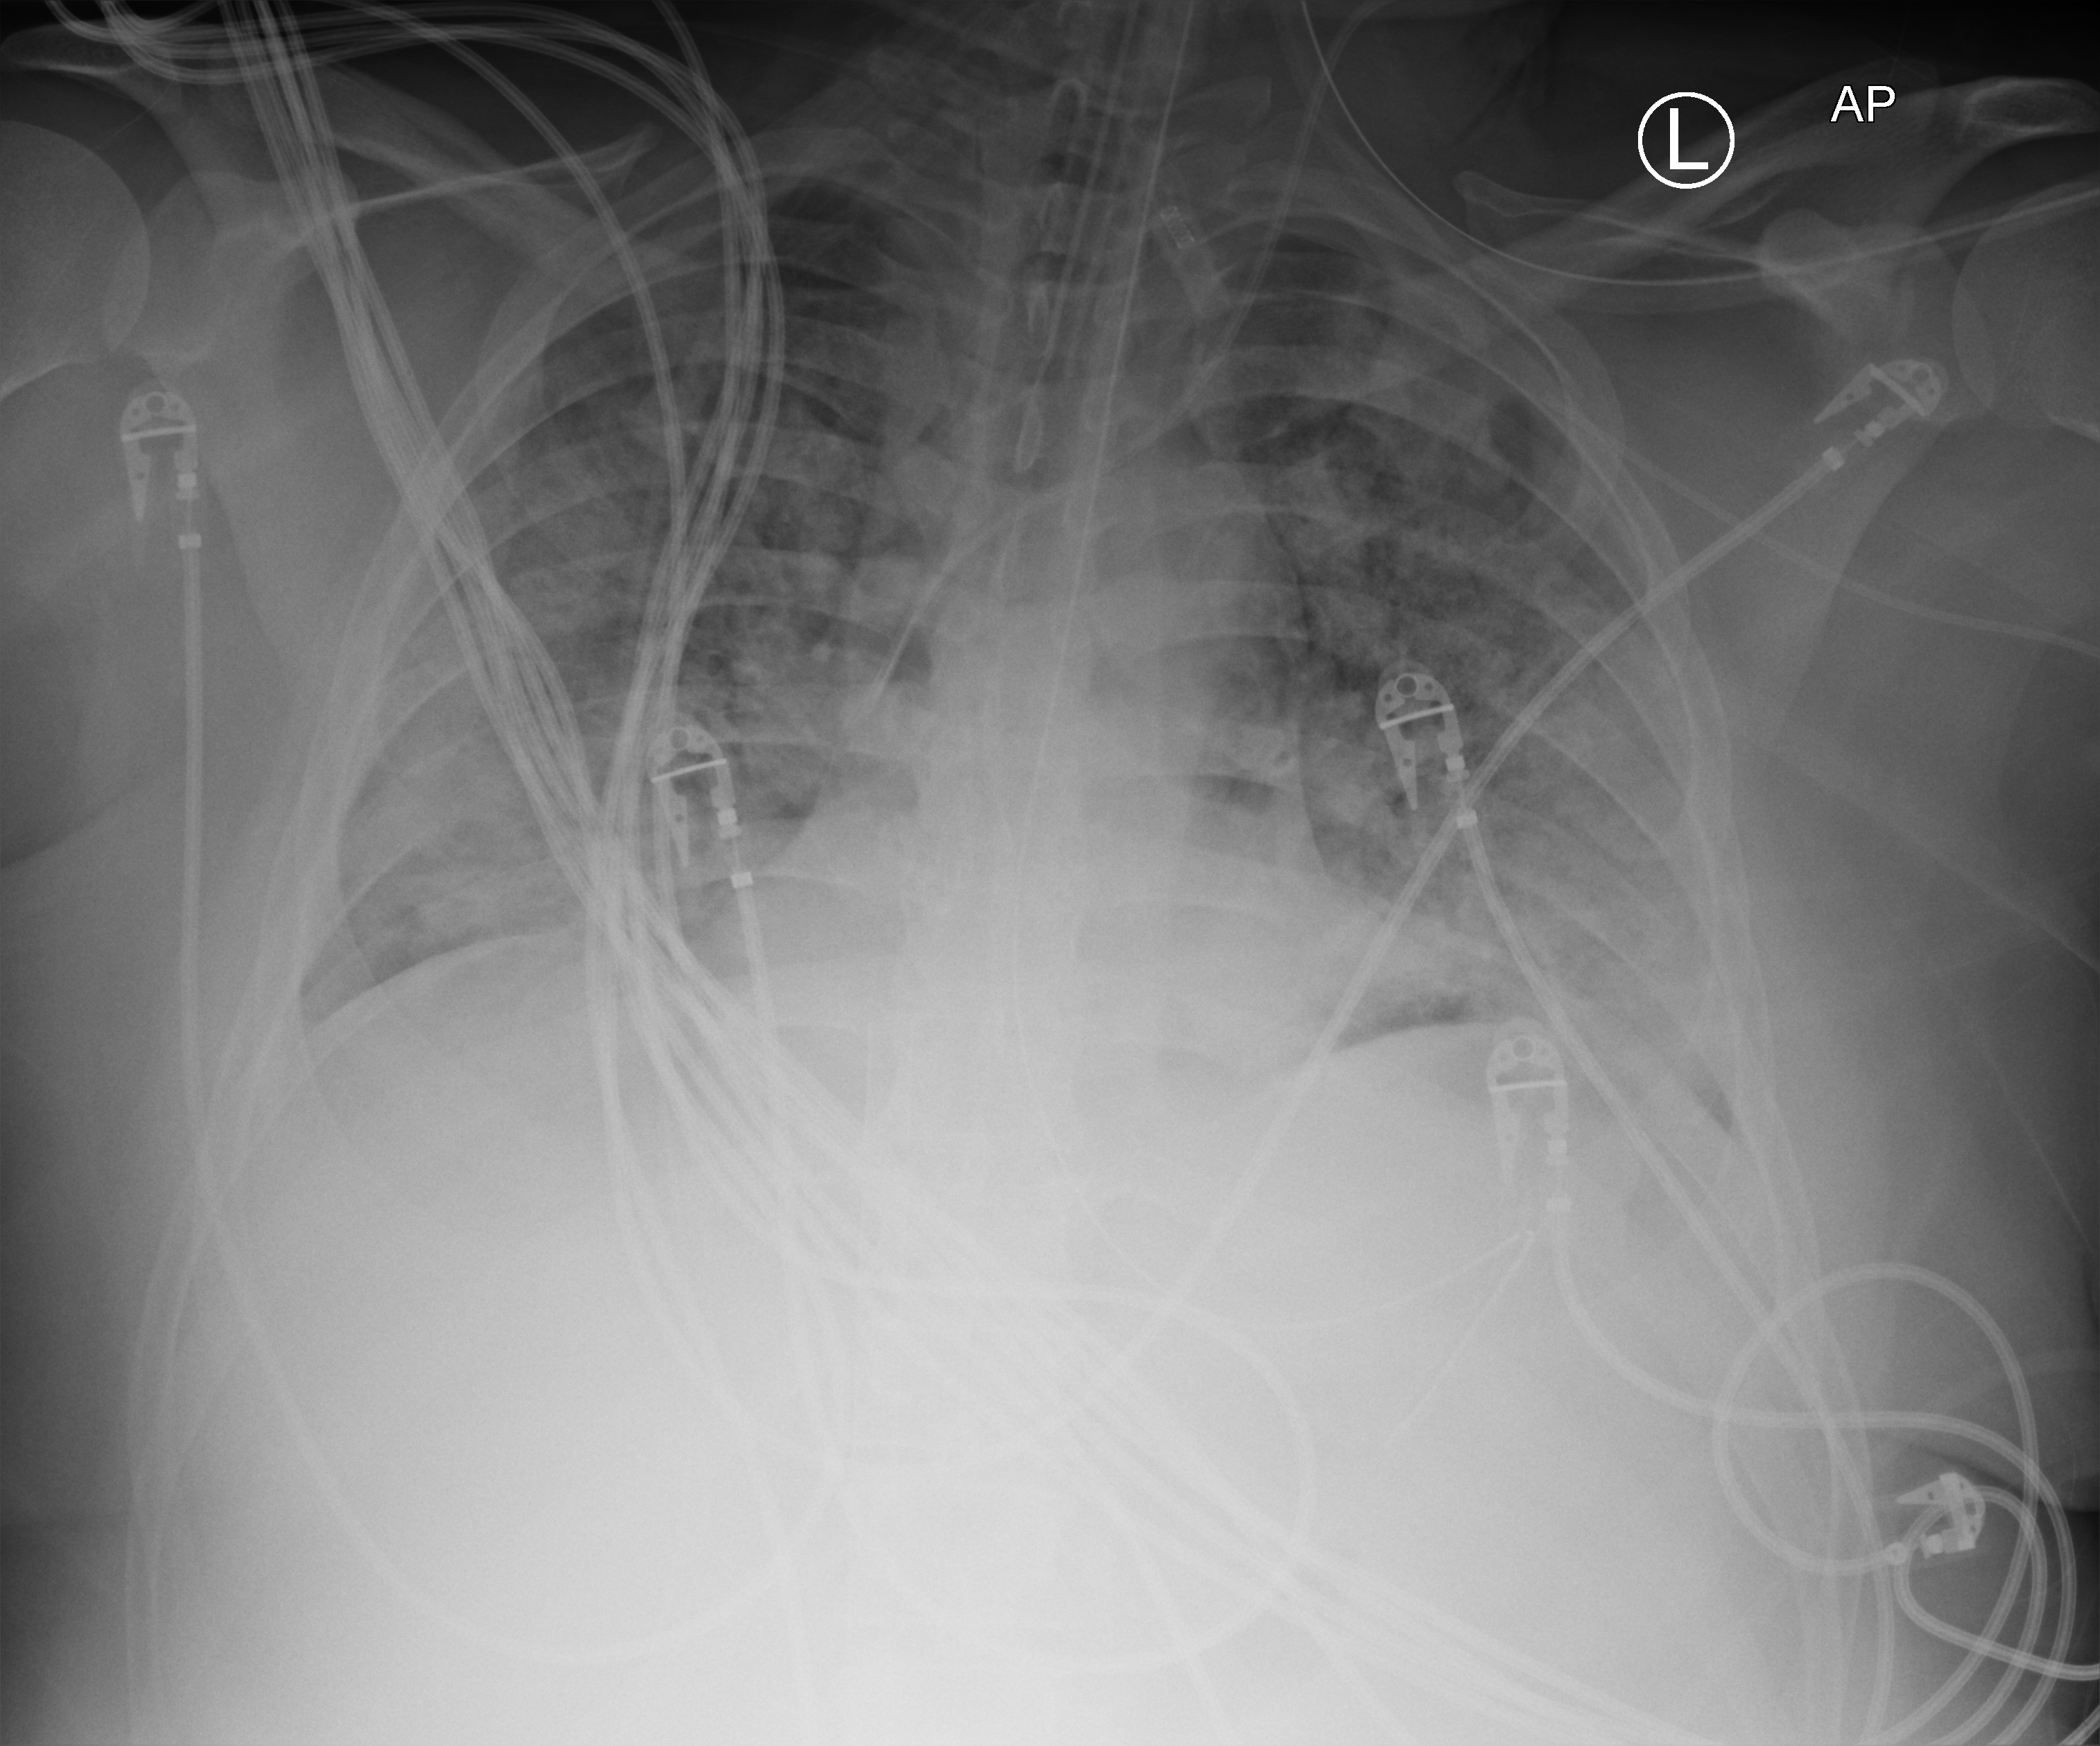
Bedside chest radiograph (computed radiography), anteroposterior (AP) projection. Adult patient hospitalised with COVID-19, age 18–59 years.
From the hospital-stay record, not from the radiograph (when in the stay this image was taken is not recorded): admitted to intensive care during this hospital stay: yes.